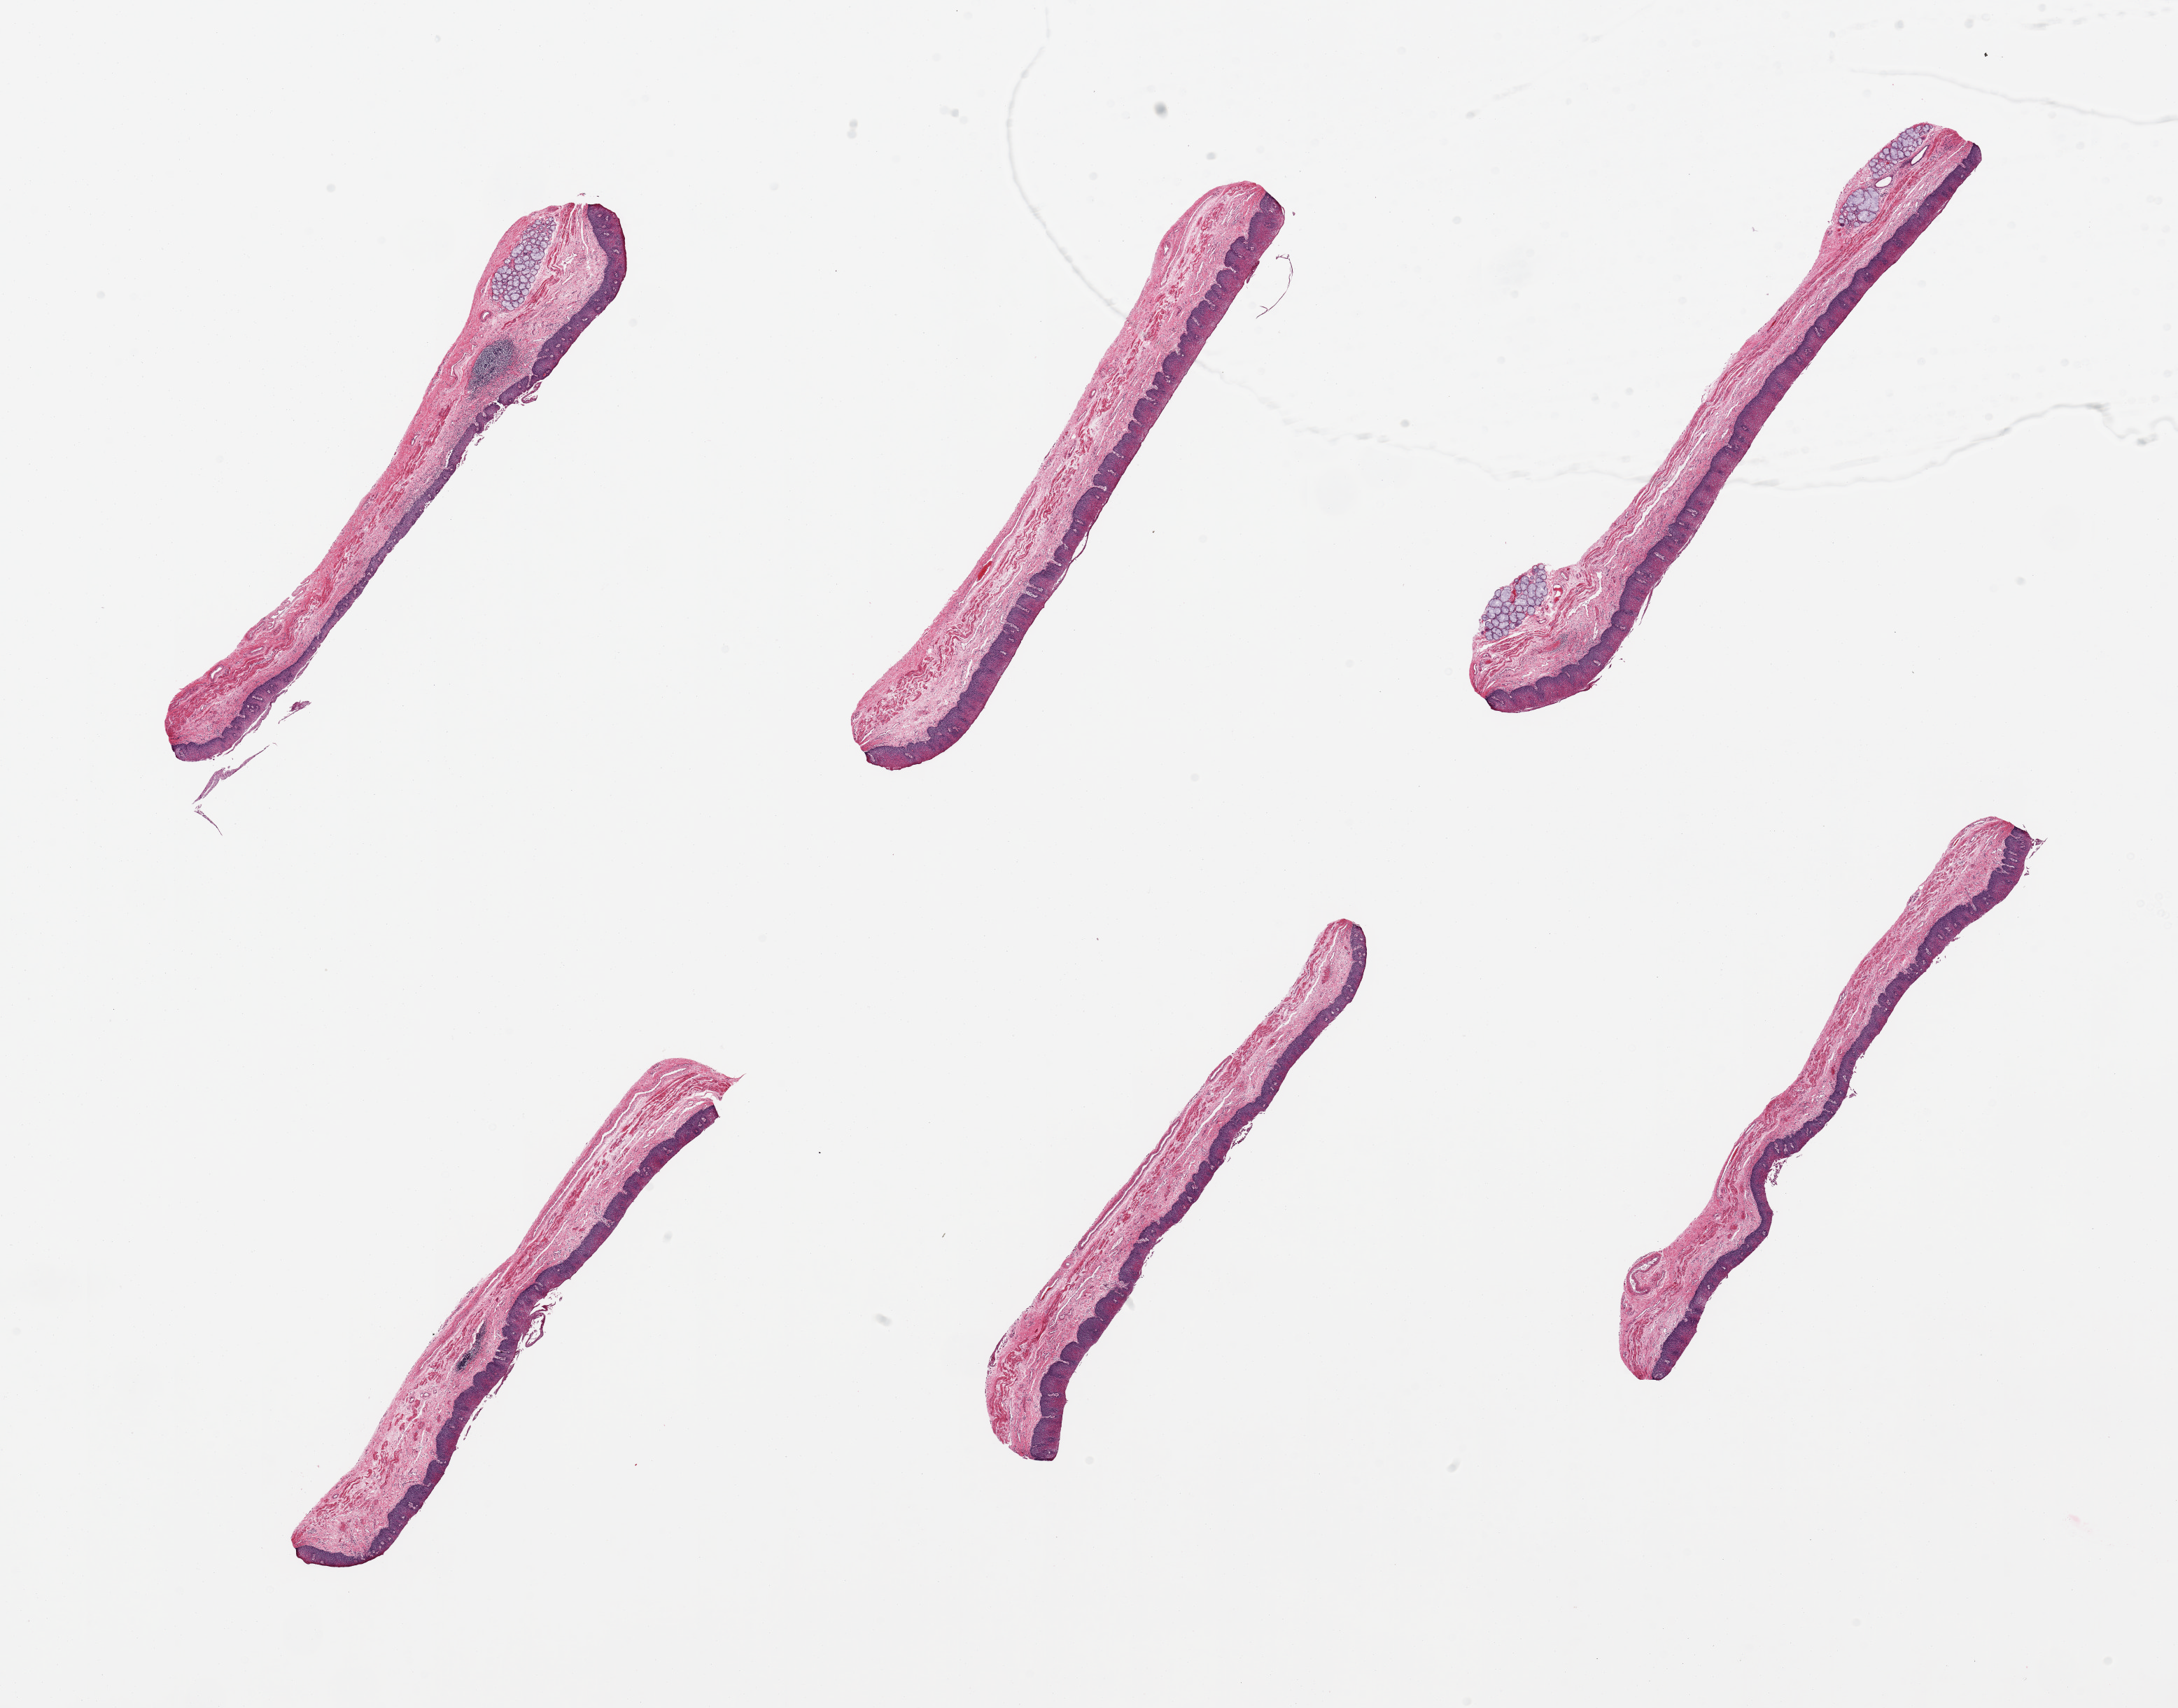
Digitized haematoxylin and eosin-stained section, brightfield — whole scanned area (about 24.6 x 19.3 mm) shown as a low-resolution overview, PAXgene-fixed paraffin-embedded (PFPE) section, target tissue: esophageal mucous membrane, donor tissue sample. Donor sex: male.
Review note (as recorded): 6 pieces, squamous mucosa up to ~0.3mm, 20-30% thickness; Few submucosal mucus glands noted.